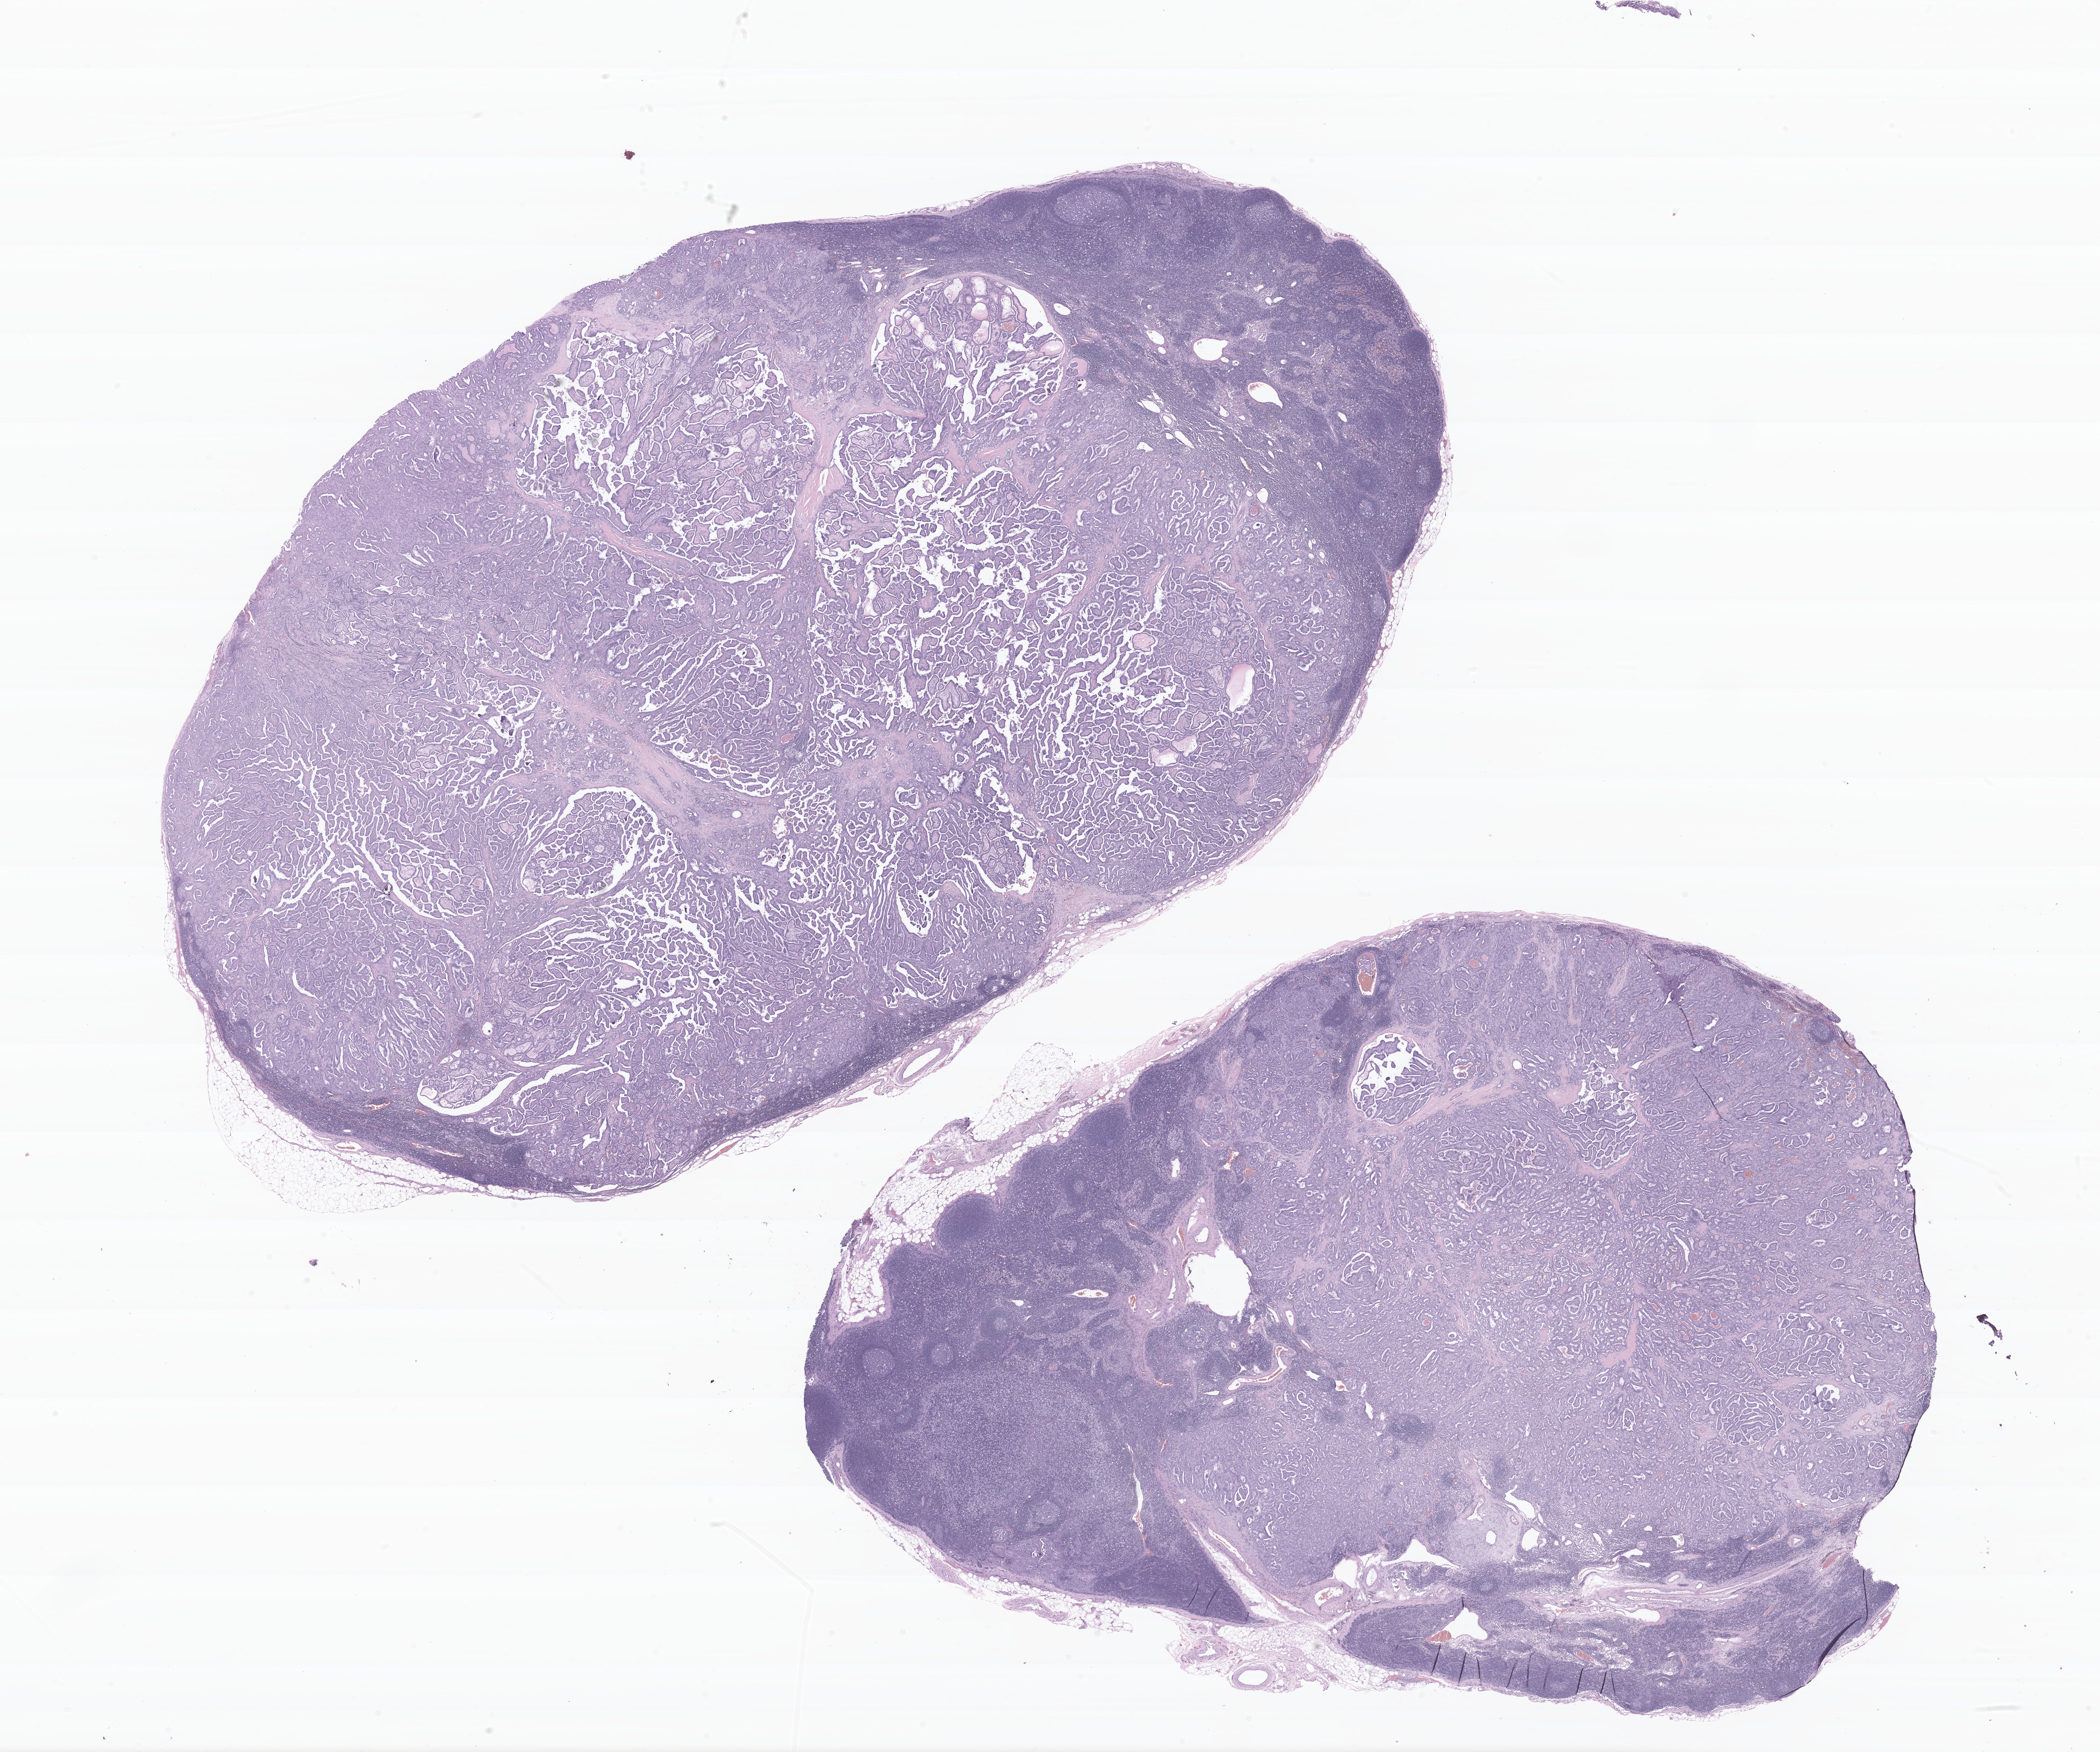
H&E whole-slide image of tumor tissue from the thyroid — a low-resolution overview of the entire scanned area, about 25.2 x 21.0 mm, formalin-fixed, paraffin-embedded (FFPE) tissue. Patient: female, age 190 months (15 years 10 months).
Recorded diagnosis: Papillary adenocarcinoma, NOS.